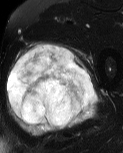
MRI of an extremity soft-tissue mass, one axial slice; position 33 of 60 along the scan axis; T2-weighted fat-saturated; MR volume resampled by the dataset authors to the PET/CT grid (not the native acquisition matrix); 123 × 153 image matrix, field of view 120 × 149 mm. Male patient. Case-level facts recorded for this patient, not image findings: histological type: pleiomorphic liposarcoma; grade: high; site of the primary tumour: left thigh.
Annotated regions visible in this slice (expert contour drawn on MRI and transferred to this co-registered scan by the dataset authors):
- gross tumour volume including surrounding oedema: bounding box <6,42,98,137> (left, top, right, bottom; pixels)
- gross tumour volume (mass): <6,43,96,128>